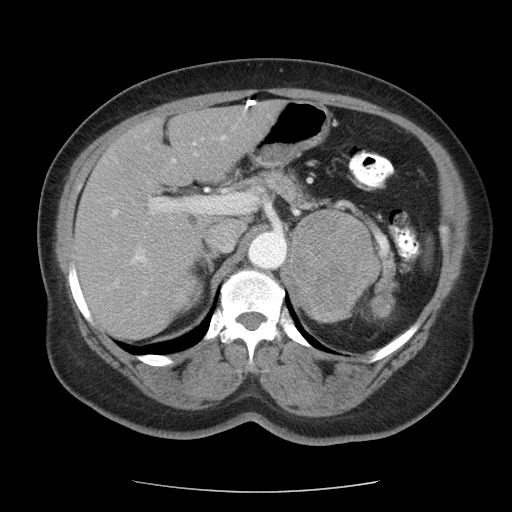
Contrast-enhanced abdominal CT, one axial slice; position 69 of 95 along the scan axis; intravenous contrast given; soft-tissue window (W 400 / L 40 HU); 5 mm slice thickness; 512 × 512 image matrix. Patient: female, 71 years. From the clinical record (not read from this slice): diagnosis: adrenocortical carcinoma; tumour side: left adrenal; tumour size at pathology: 8.8 cm; Ki-67 index: 20 %; stage (as recorded): 2.
Outlined on this slice (semi-automatic segmentation, software-assisted and operator-edited):
- mass: box from (x=286, y=211) to (x=382, y=322) px